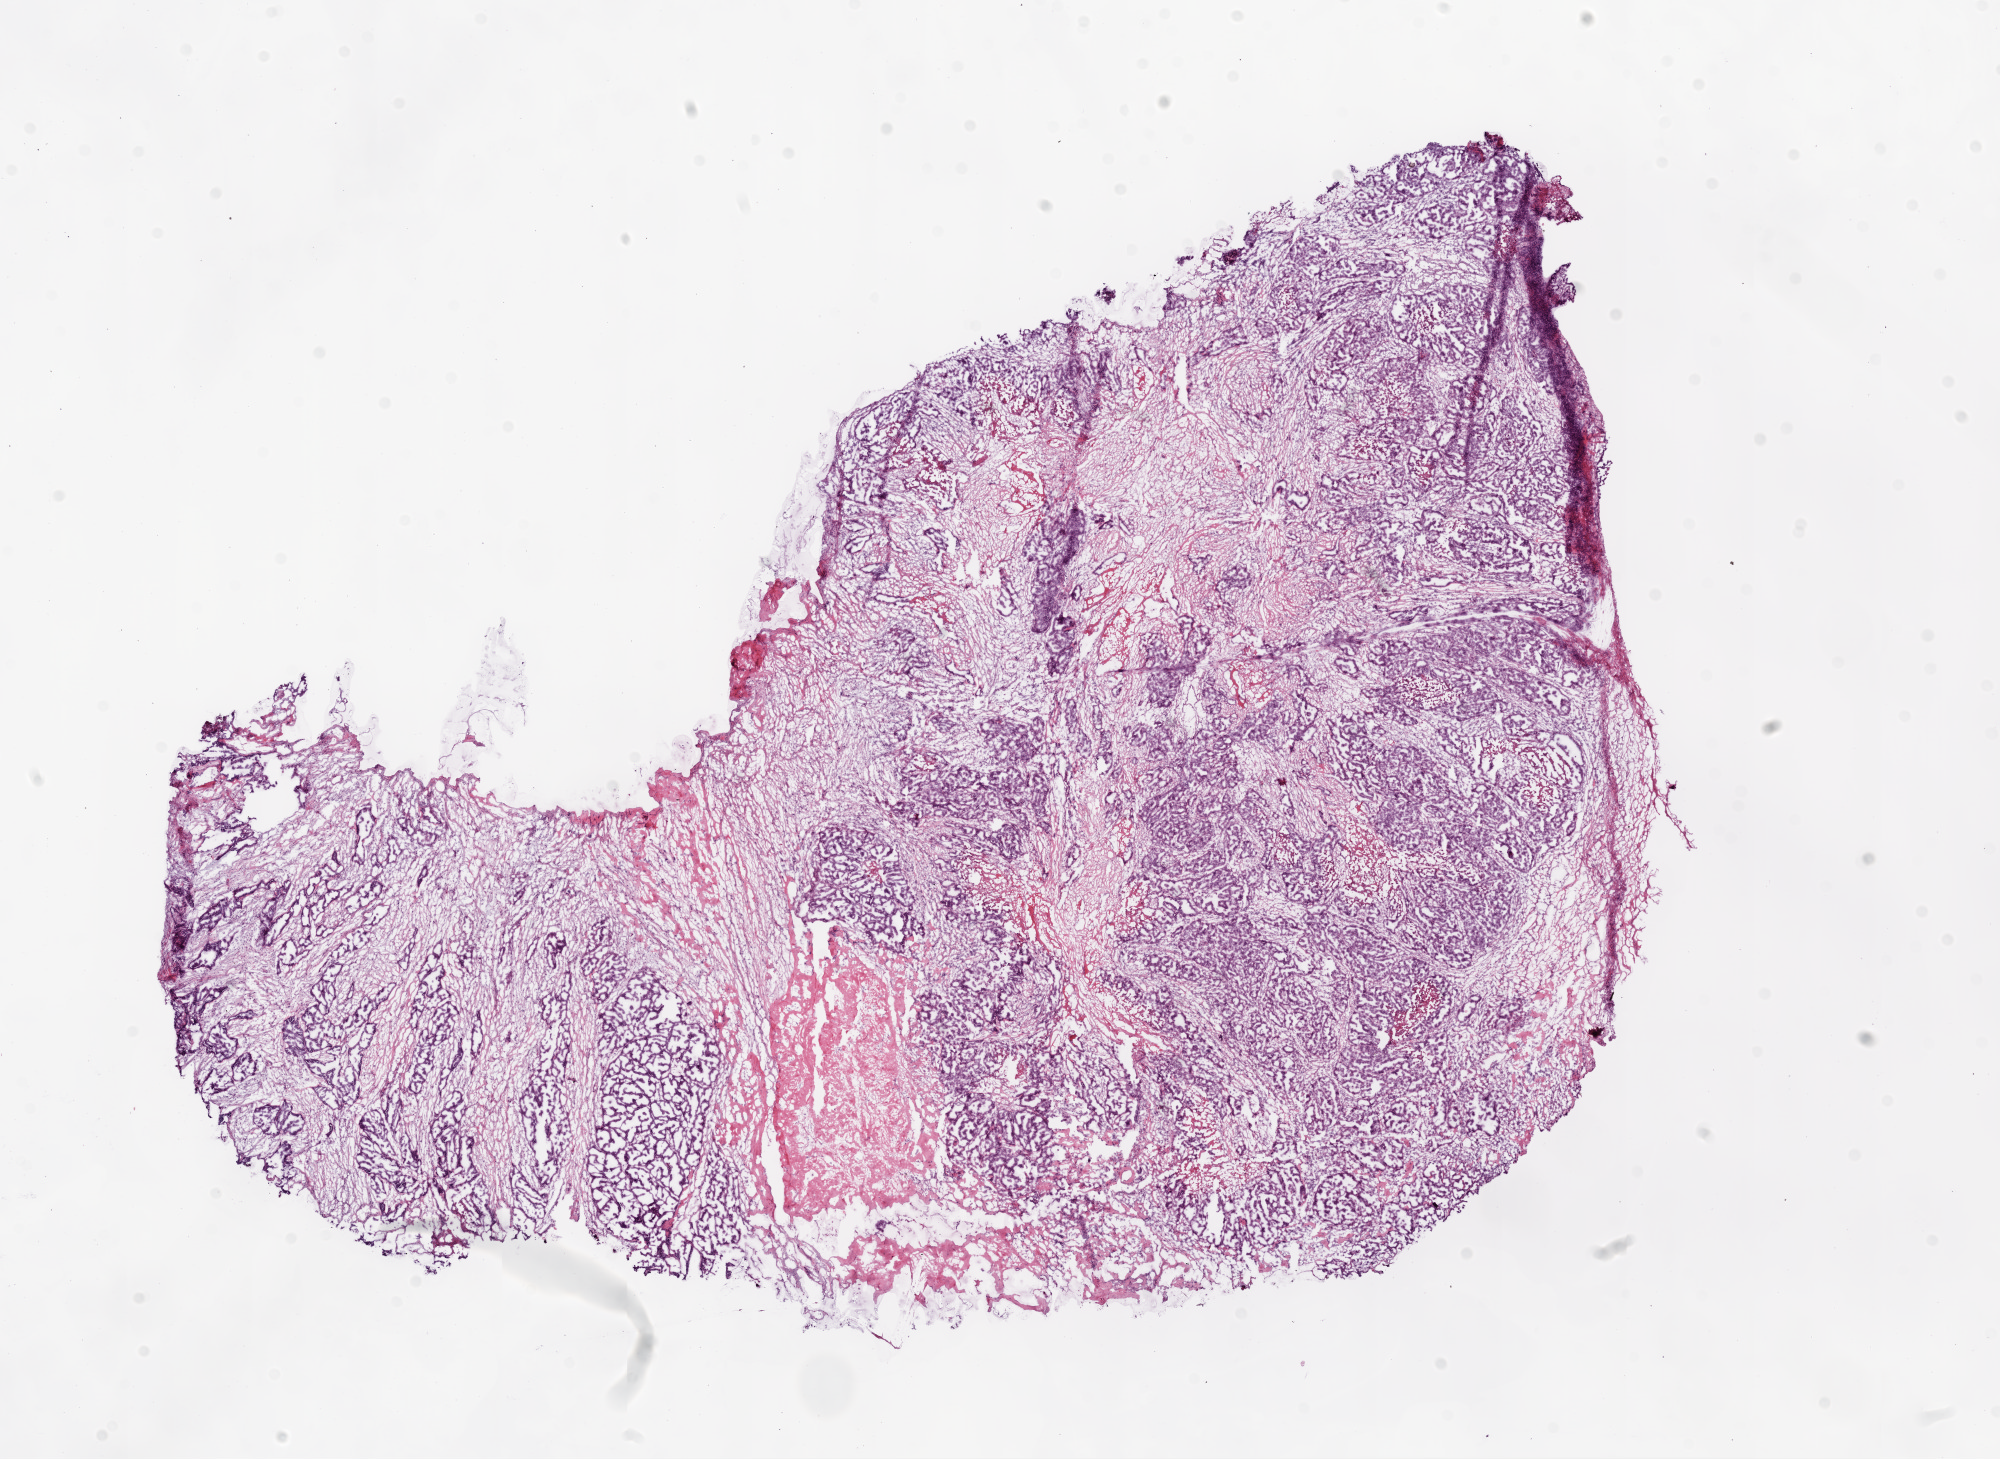
H&E-stained whole-slide image, low-resolution overview of the scanned area, about 16.0 x 11.7 mm (slide scanned at 20x), frozen section from the top of the tissue portion, sample: primary tumour, ovary. Female, age 68 years at initial diagnosis. Histologic grade: G3 (poorly differentiated). Pathologist review of this section (percent, as recorded): tumour cells 70%, tumour nuclei 70%, normal cells 0%, stromal cells 25%, necrosis 5%.
* diagnosis: Serous cystadenocarcinoma, NOS
* FIGO stage: IIA
* laterality: bilateral